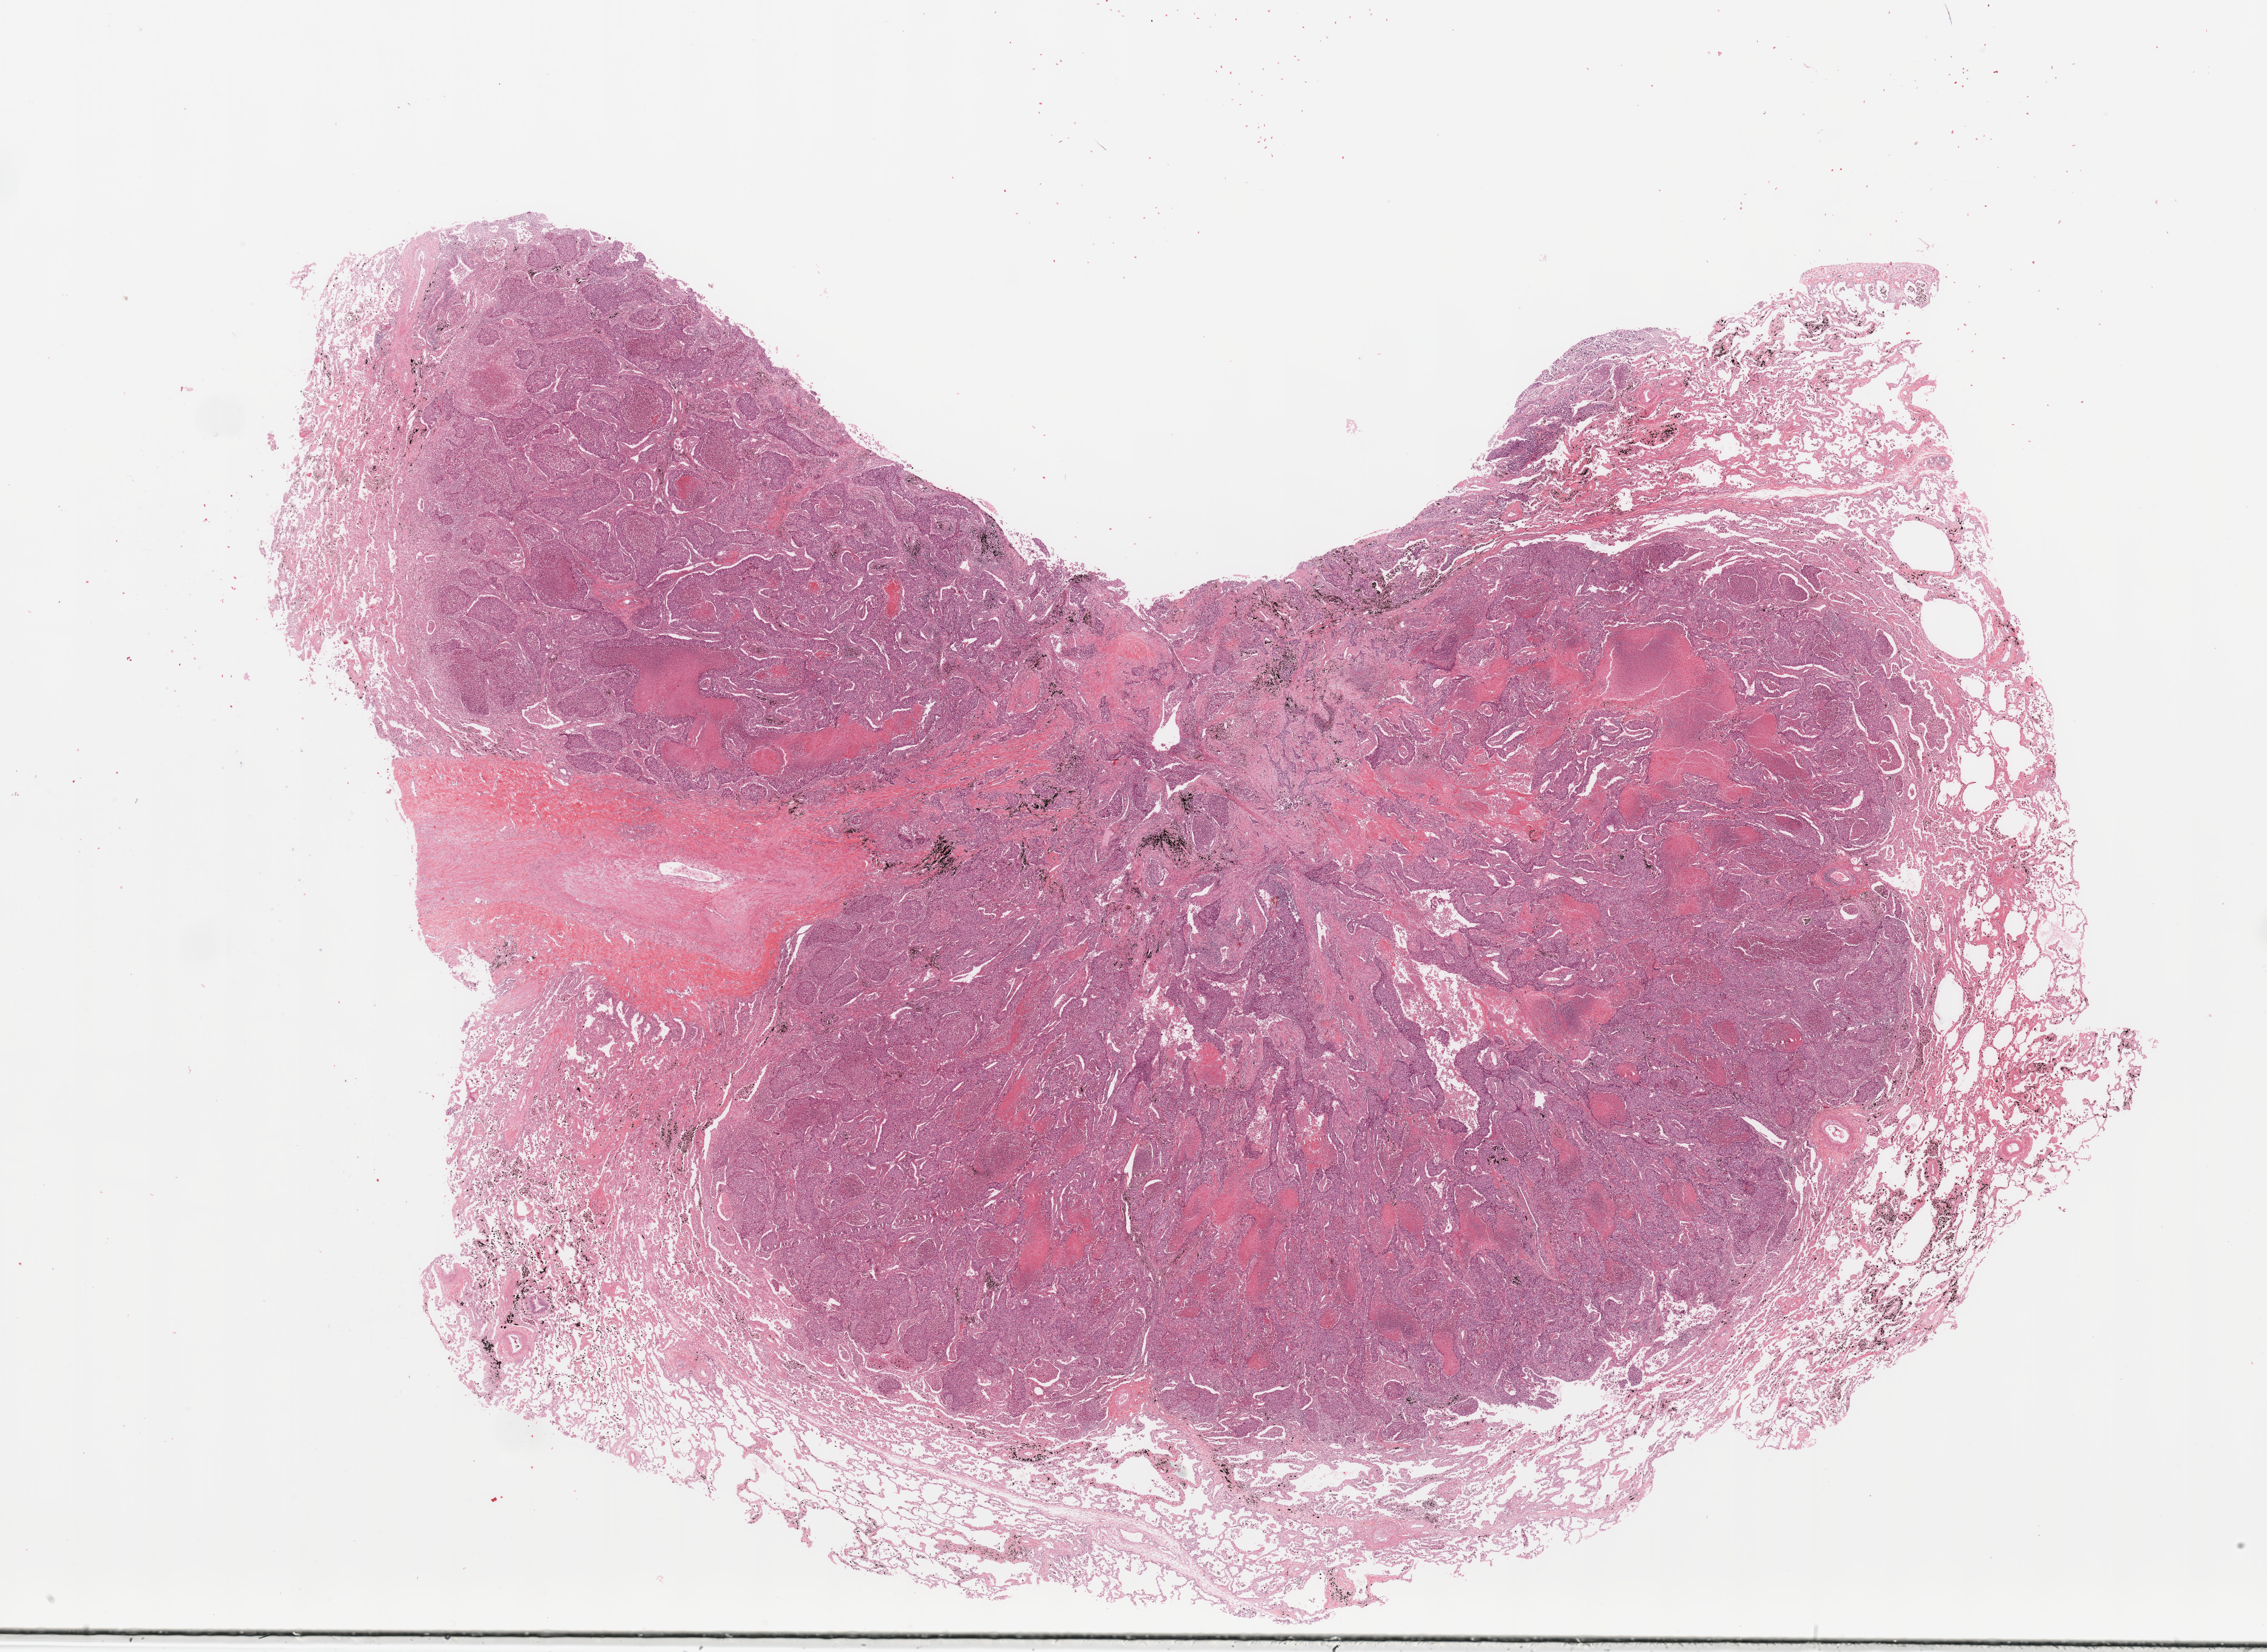
Hematoxylin and eosin (H&E) stained whole-slide image — whole scanned area (about 29.5 x 21.5 mm, acquisition: 20x scan) shown as a low-resolution overview. Tumour tissue sample, sampled site: lung. Patient: male, age 65 years. Histologic grade: G3 (poorly differentiated). Slide review estimates, as recorded: tumour nuclei 70%, necrosis 15%.
AJCC pathologic stage: IB. Diagnosis: Squamous cell carcinoma, NOS.